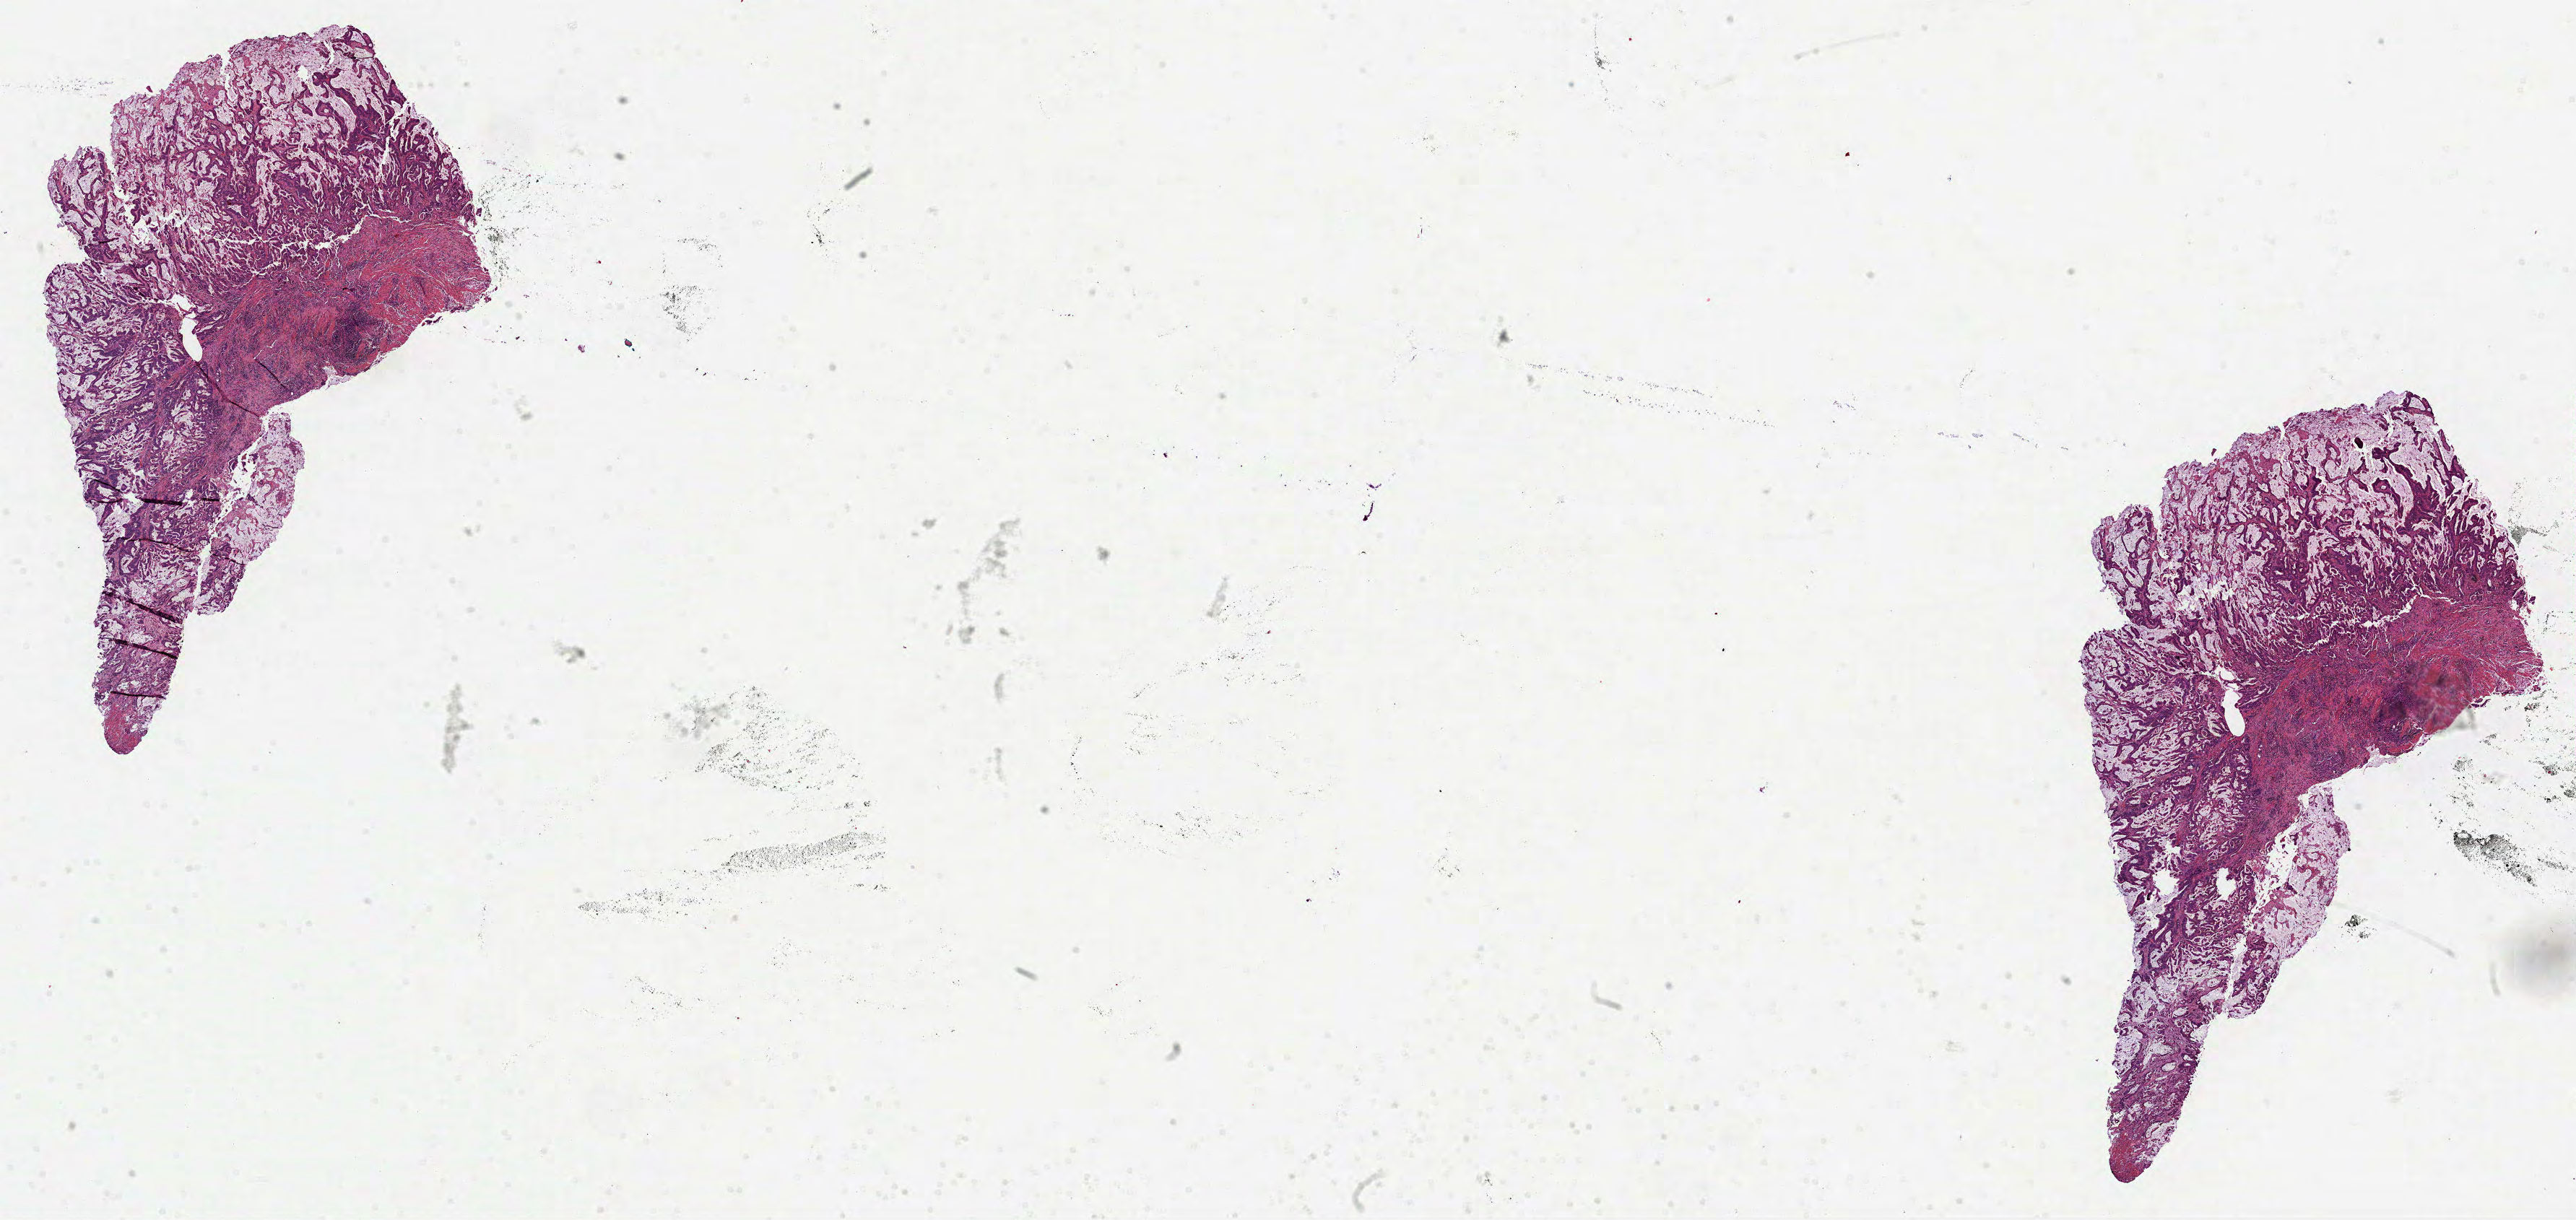
Whole-slide histology image, H&E, whole scanned area (about 28.8 x 13.6 mm) shown as a low-resolution overview; FFPE section; primary tumour sample from the colon. Female patient; age at initial diagnosis 84 years.
Diagnosis: Adenocarcinoma, NOS (ascending colon).